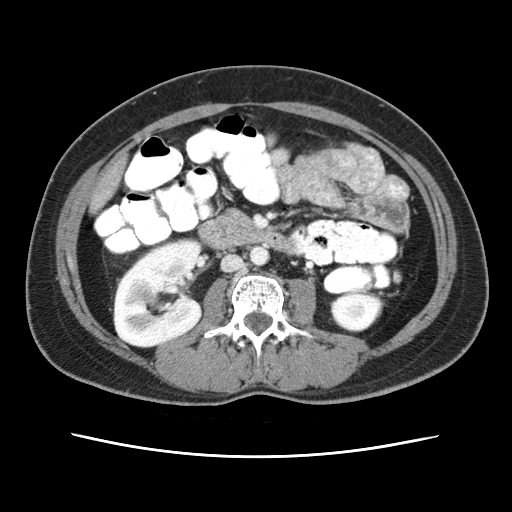
Contrast-enhanced abdominal CT (liver protocol), one axial slice. Slice 4 of 79 in the series (ordered by position). Reconstruction kernel STANDARD. 120 kVp. Soft-tissue window (W 400 / L 40 HU). 2.5 mm slice thickness. 512 × 512 image matrix, field of view 340 × 340 mm. Case-level facts recorded for this patient, not image findings: diagnosis: hepatocellular carcinoma (patient treated with transarterial chemoembolisation; whether this scan precedes or follows treatment is not stated here); TNM stage (as recorded): Stage-I.
Outlined on this slice (semi-automatic segmentation, software-assisted and operator-edited):
- abdominal aorta: bounding box <251,247,268,266> (left, top, right, bottom; pixels)
- liver parenchyma outside the tumour (the mass and vessels are separate outlines, so this box may not span the whole liver): <90,158,124,210>